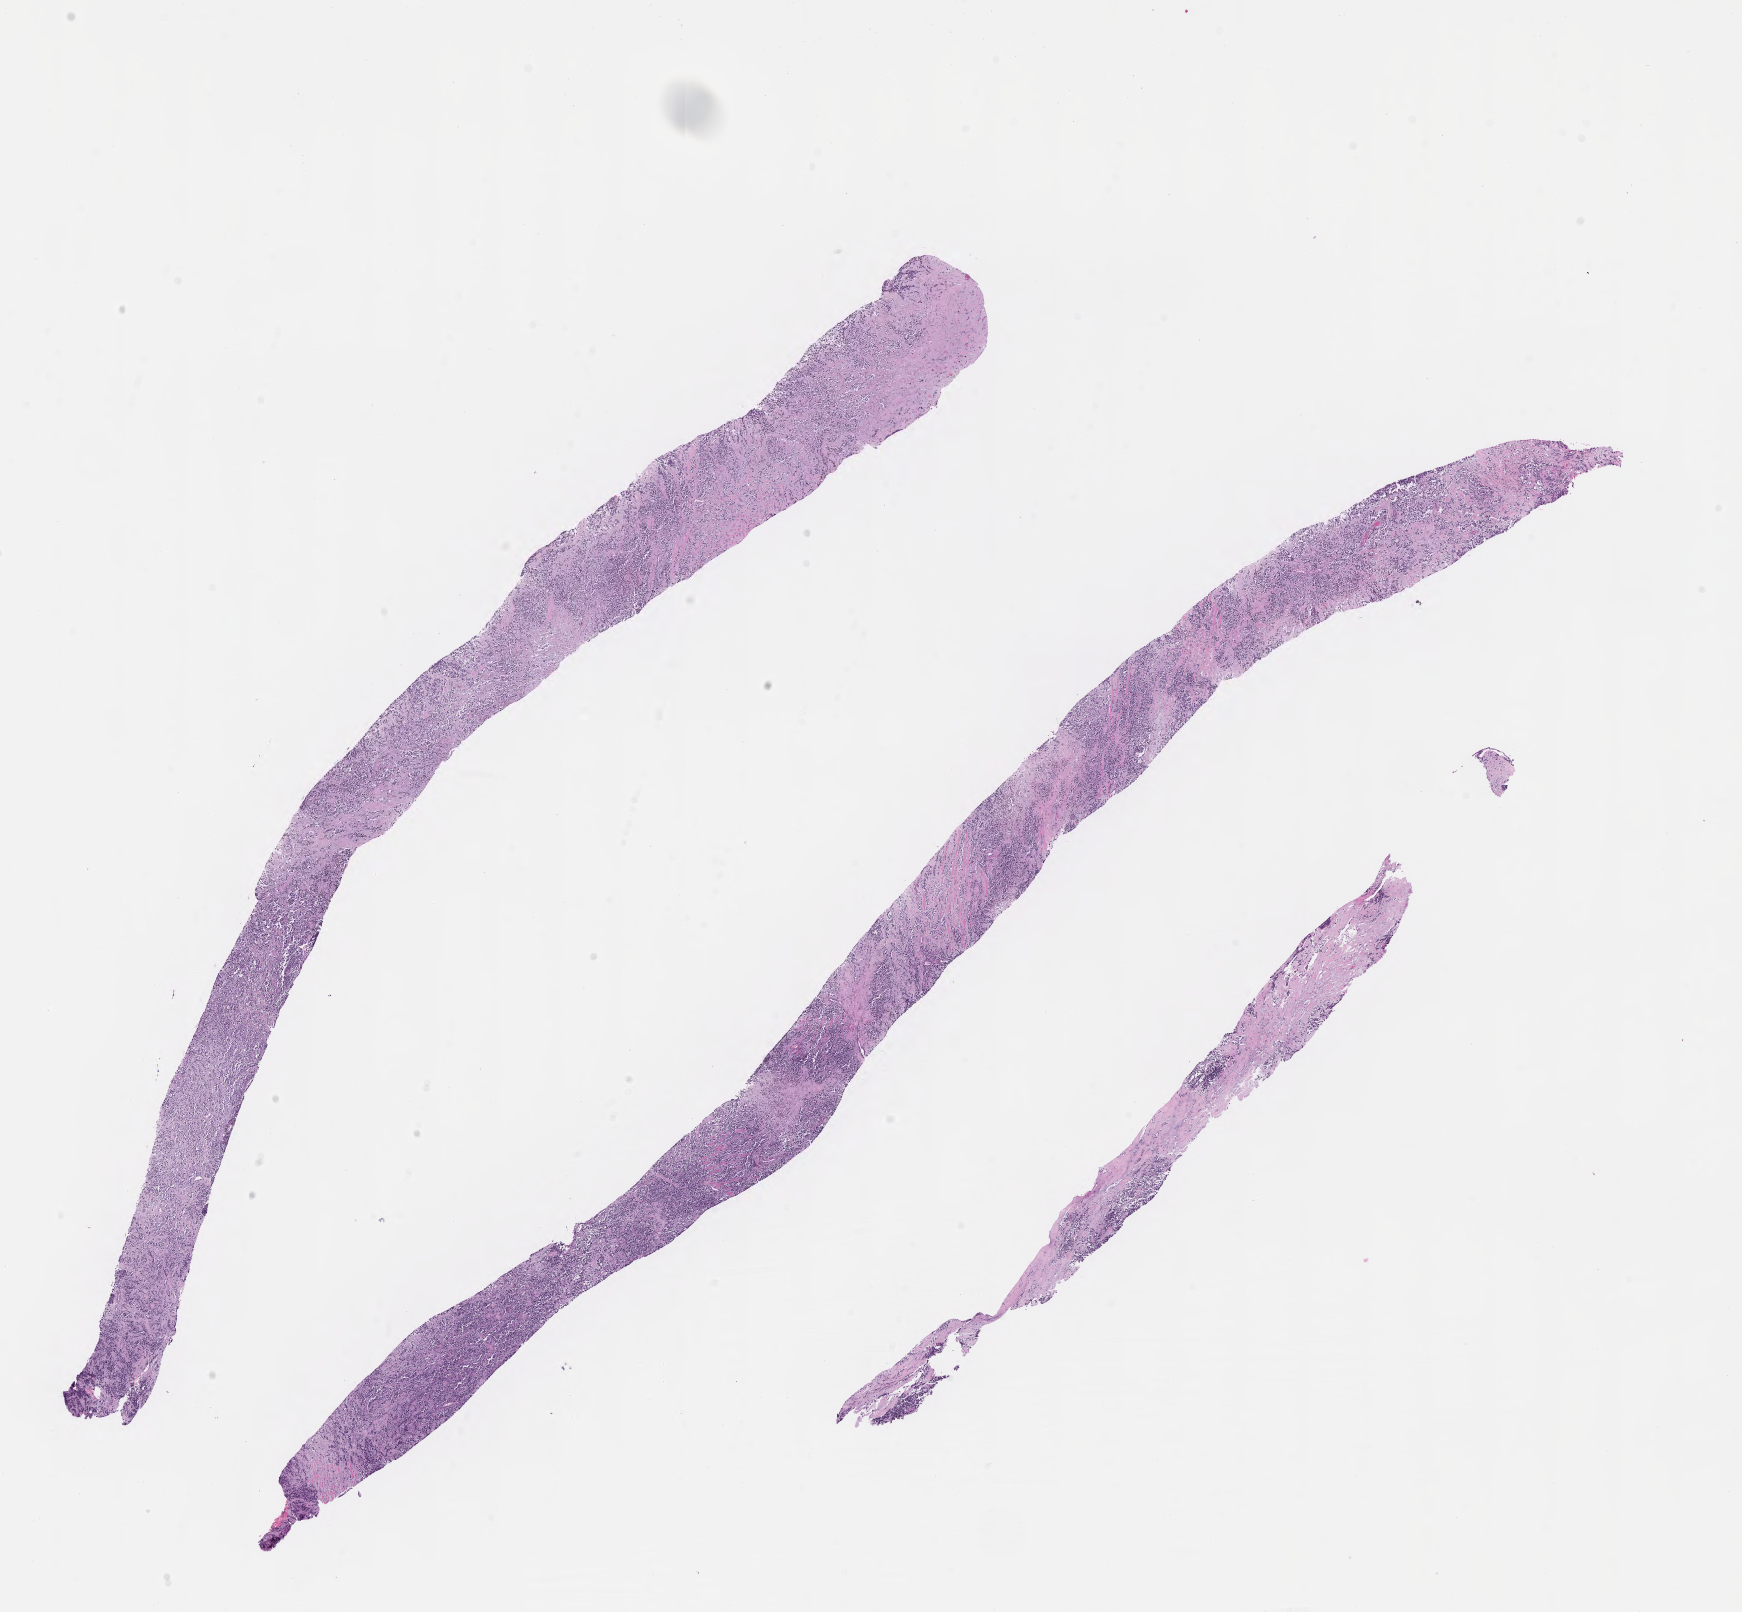
Whole-slide image, hematoxylin and eosin (H&E) stain of tumor tissue from the upper limb, whole scanned area (about 14.1 x 13.0 mm) shown as a low-resolution overview, formalin-fixed paraffin-embedded section. Patient male; age 906 days (about 2.5 years).
Recorded diagnosis: Alveolar rhabdomyosarcoma.